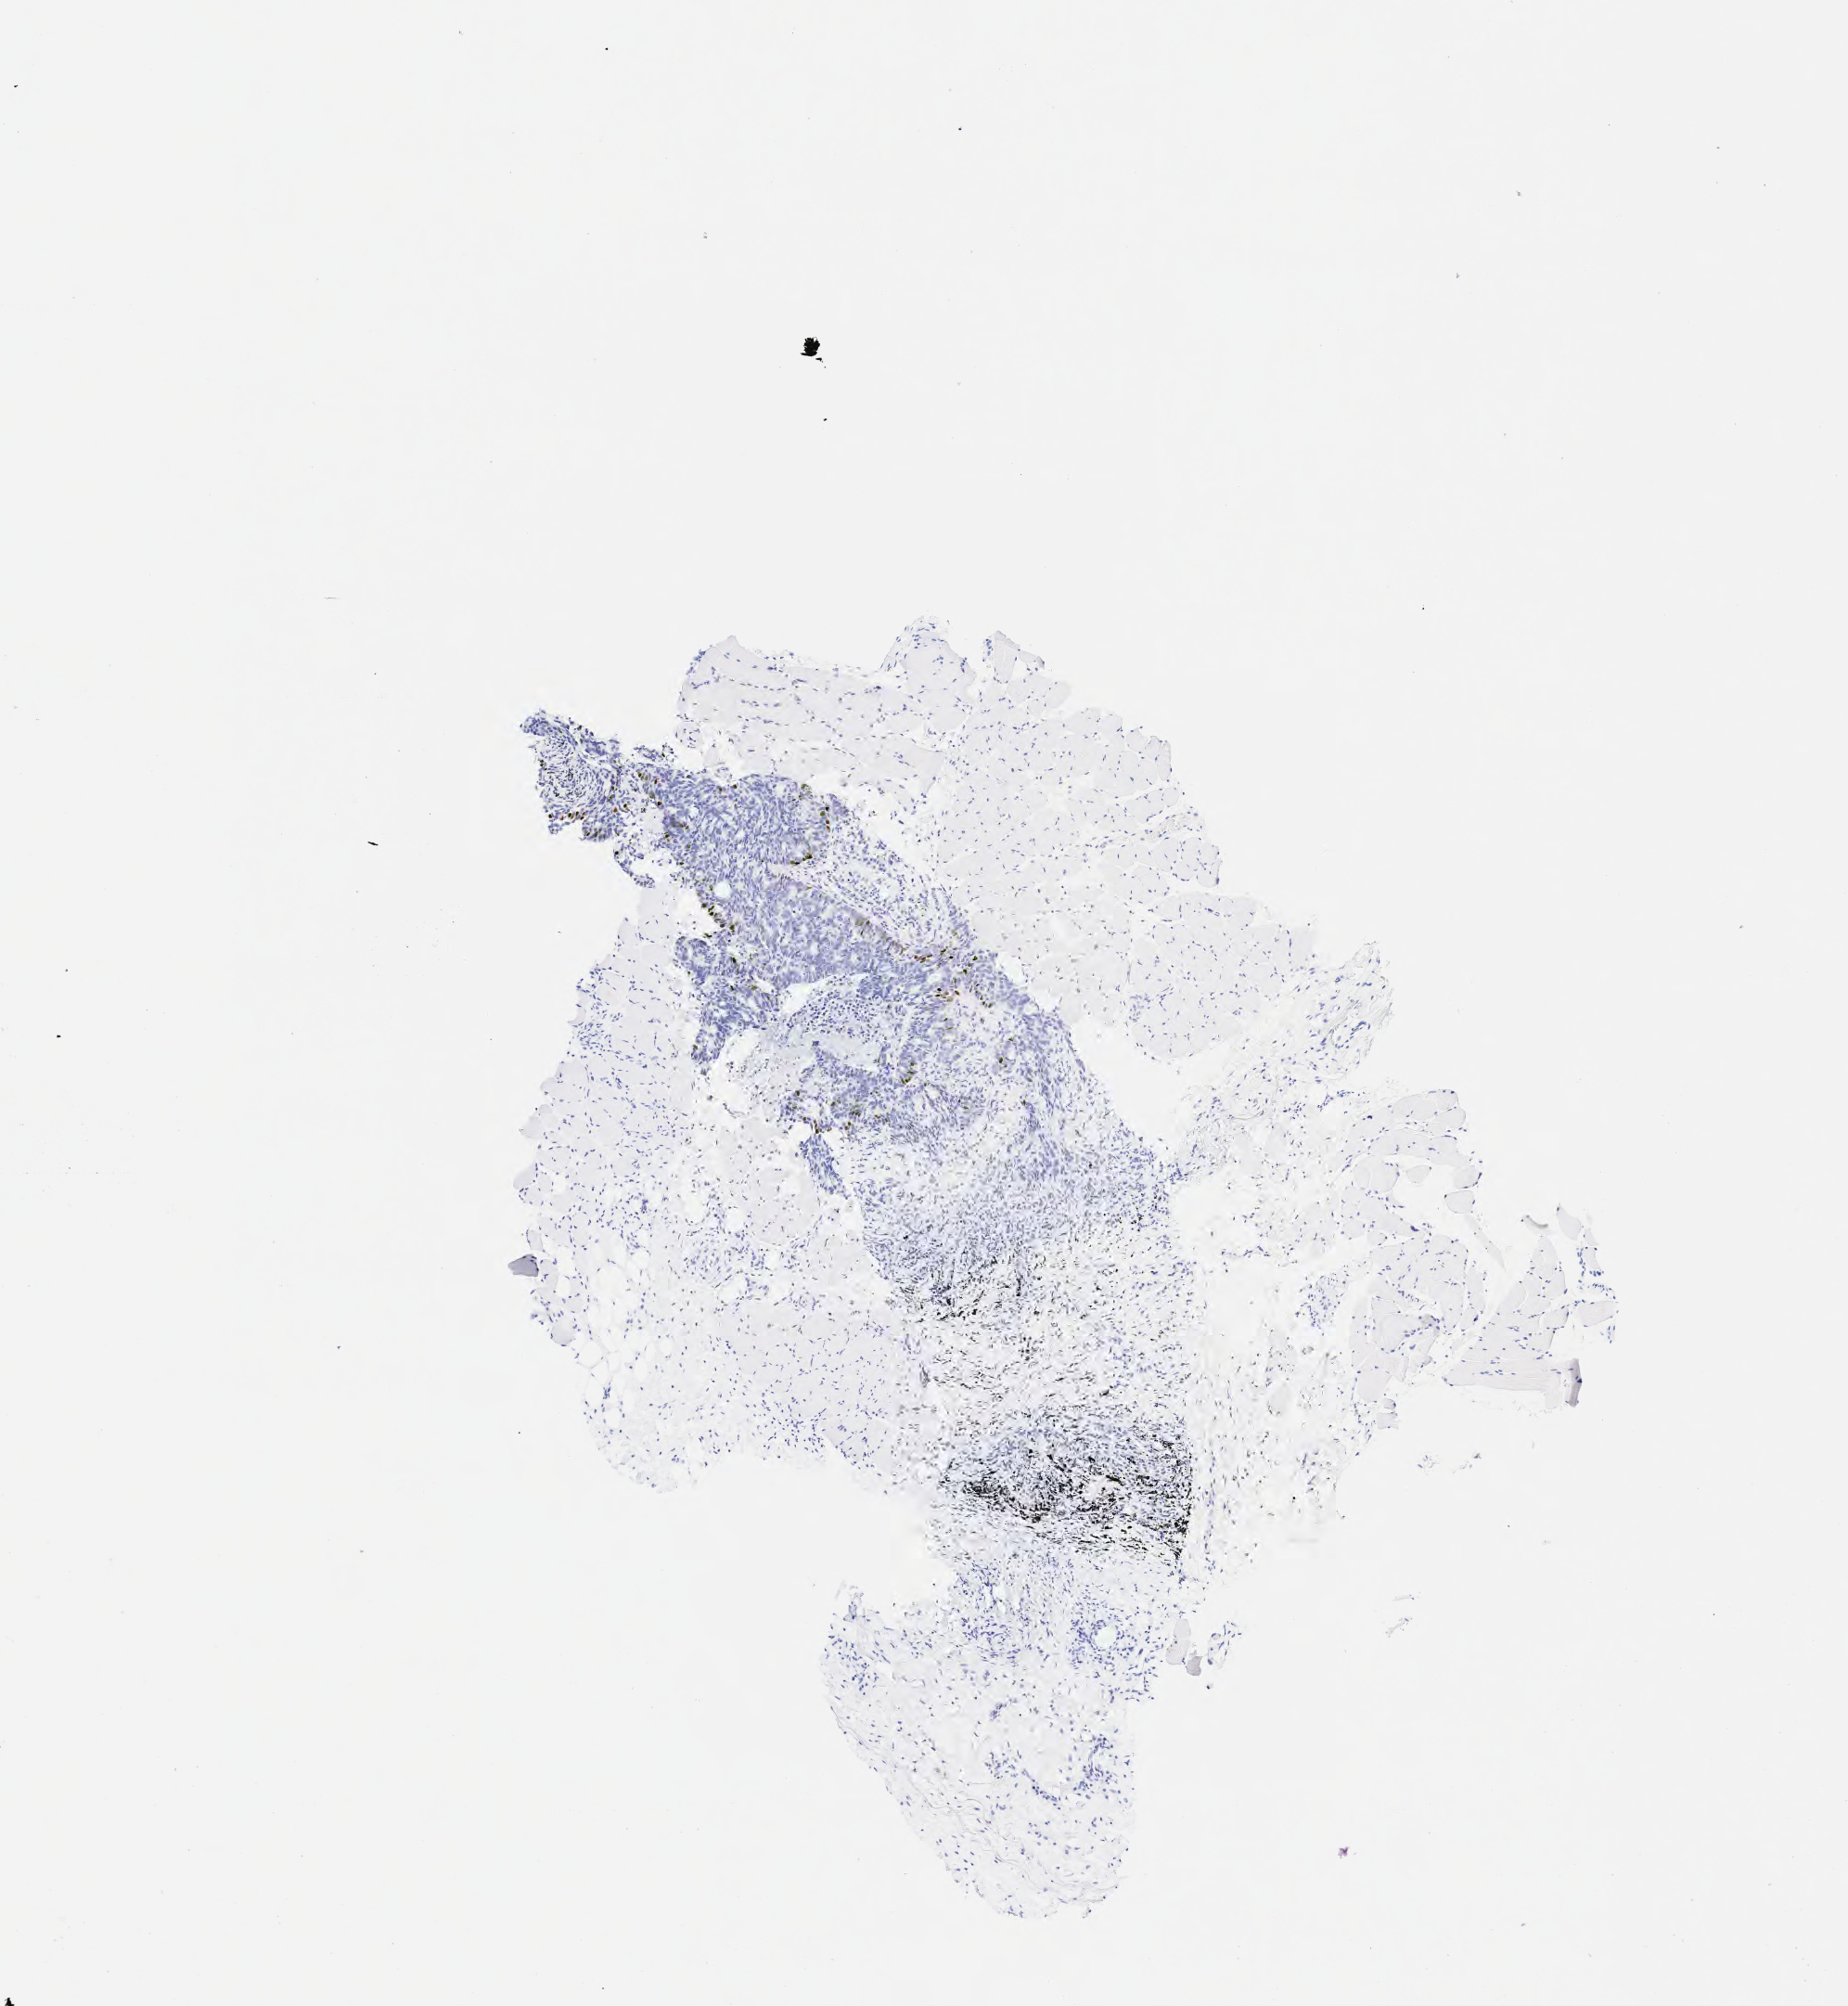
Immunohistochemistry (IHC) whole-slide image stained for p40, shown as a low-resolution overview of the whole scanned area (about 4.0 x 4.4 mm), specimen: tumor tissue, site: lung. Patient: female, 68 years old.
Histologic diagnosis: Squamous cell carcinoma, large cell, nonkeratinizing, NOS.